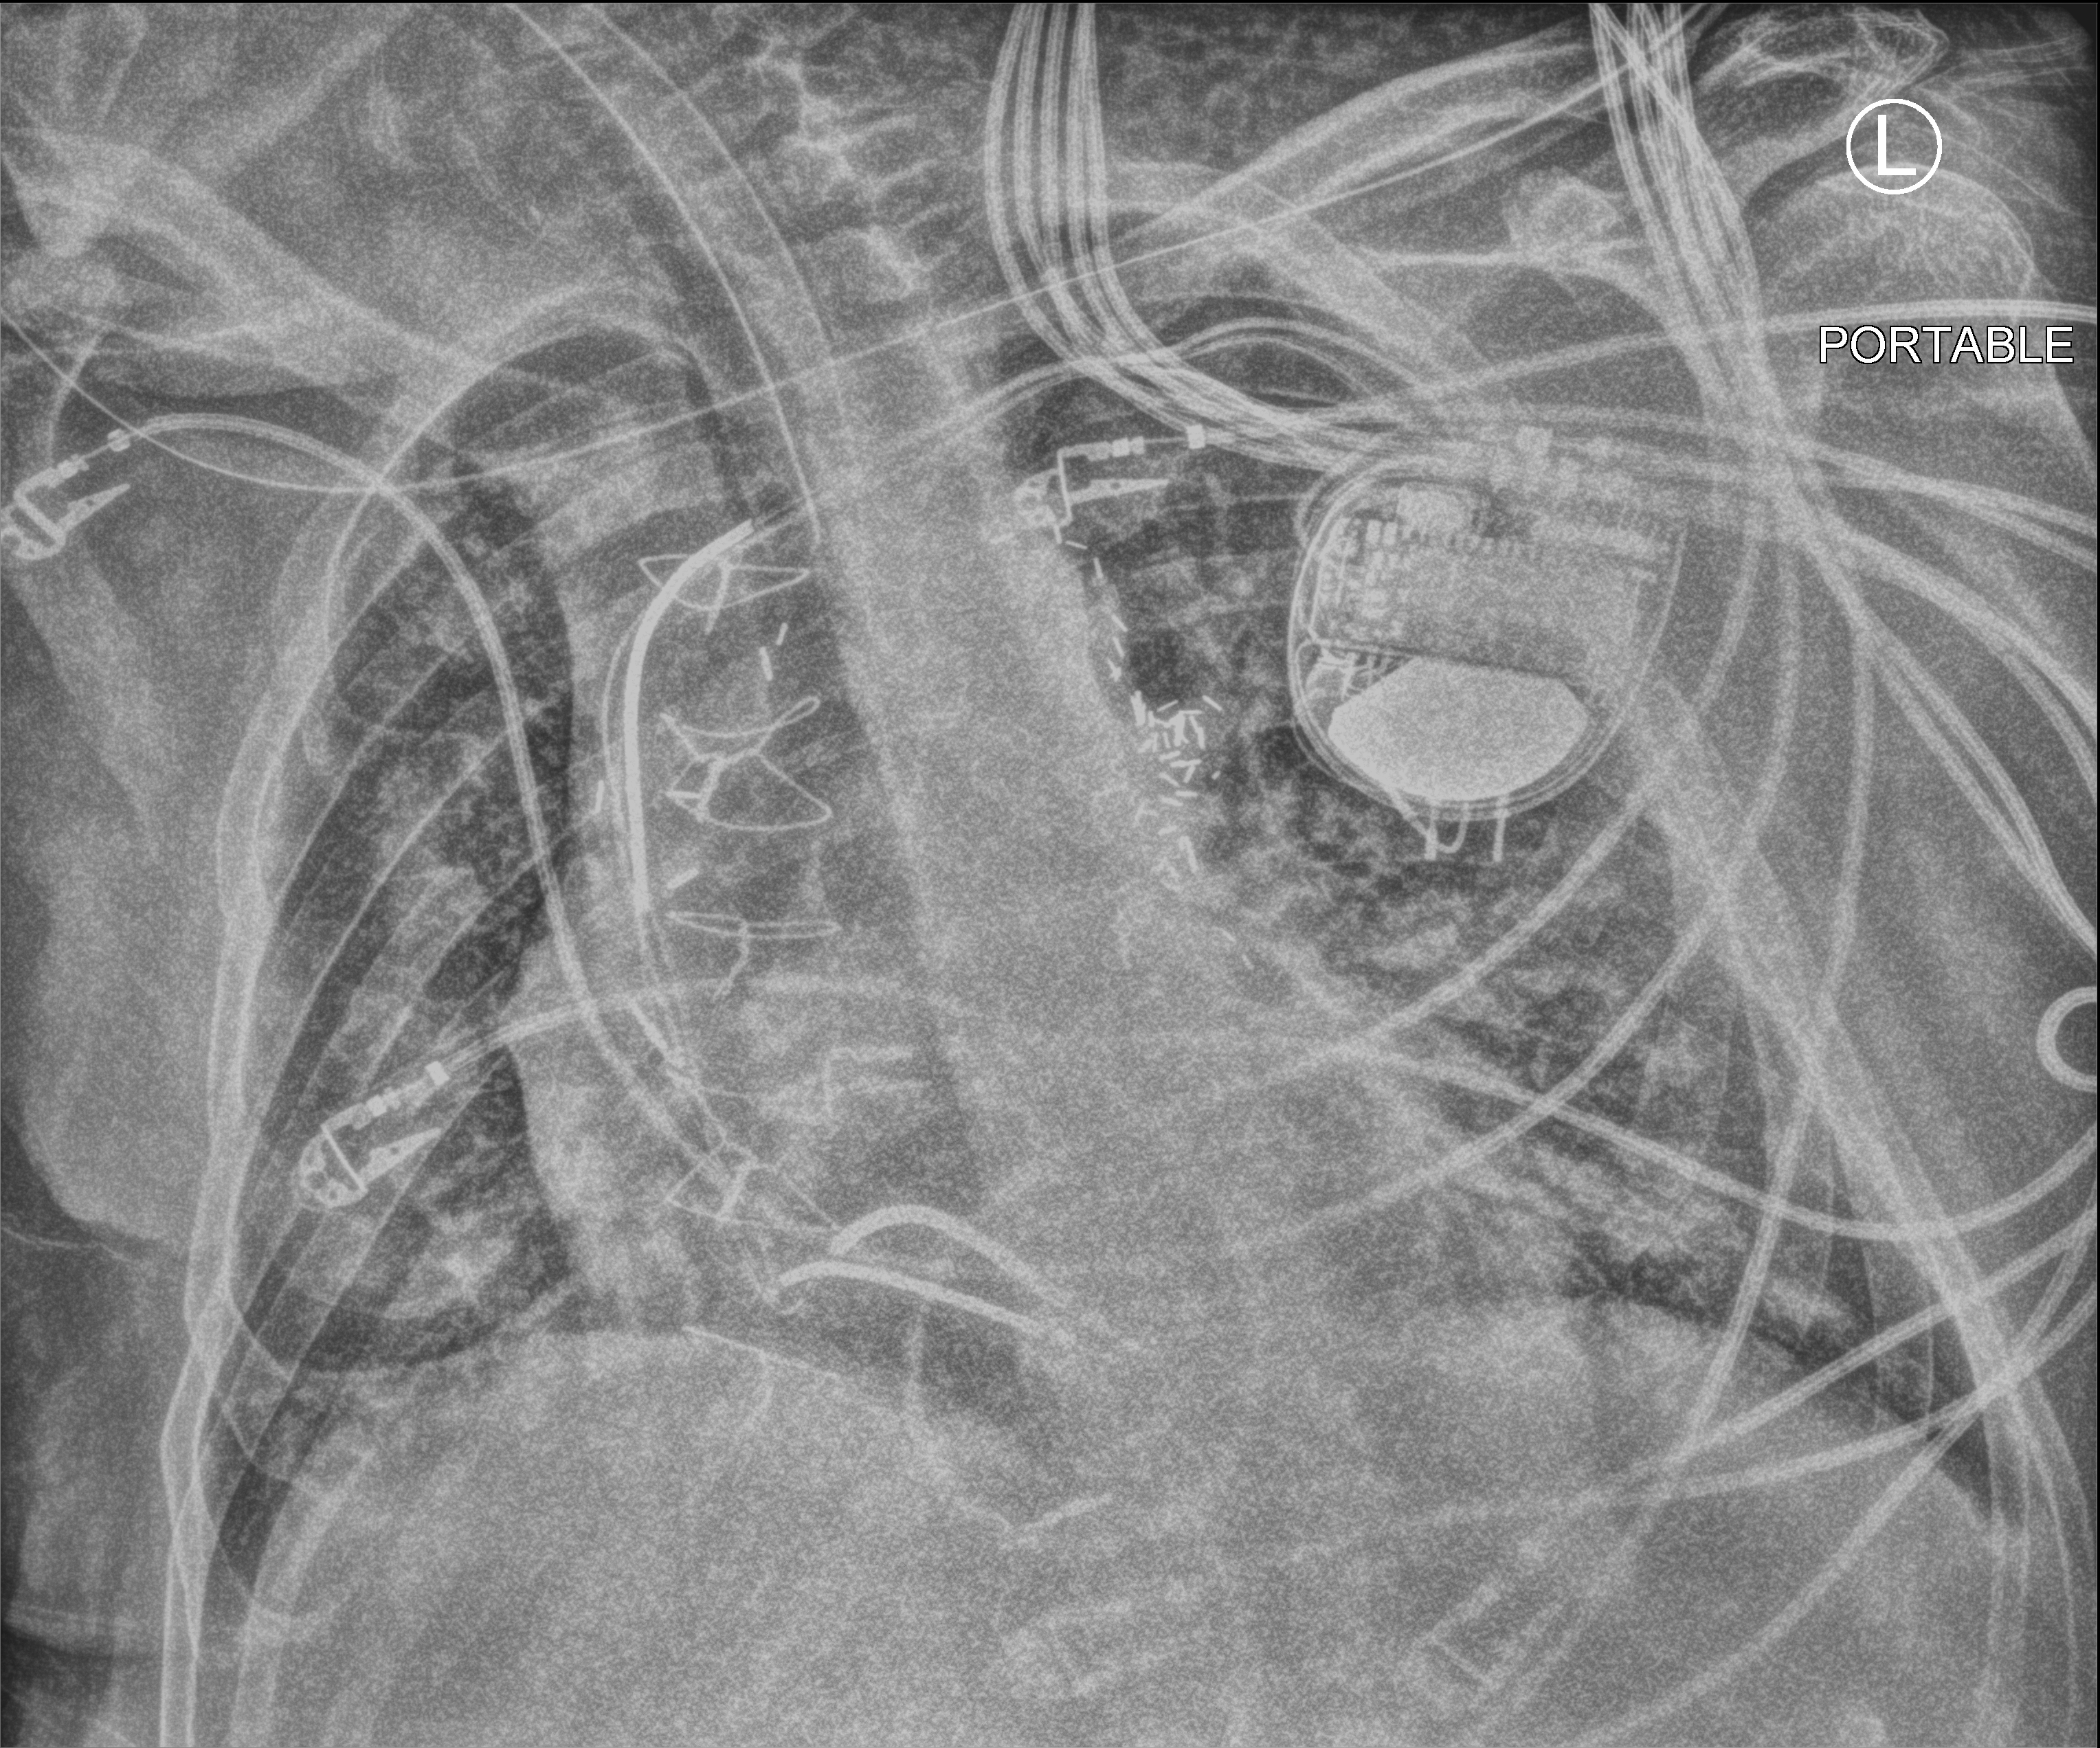
Chest X-ray (portable); anteroposterior (AP) projection. Patient hospitalised with COVID-19; male, aged 60–74 years.
Admission-level facts for this patient (not findings on this image; timing relative to this image not recorded):
- admitted to intensive care during this hospital stay: yes
- mechanically ventilated during this hospital stay: yes